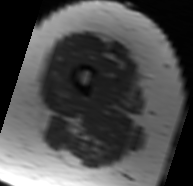
MRI of an extremity soft-tissue mass, one axial slice; position 11 of 91 along the scan axis; MR volume resampled by the dataset authors to the PET/CT grid (not the native acquisition matrix); 193 × 186 image matrix, field of view 188 × 182 mm. Female patient. Case-level facts recorded for this patient, not image findings: histological type: malignant solitary fibrous tumor; grade: intermediate; site of the primary tumour: right thigh.
Annotated regions visible in this slice (expert contour drawn on MRI and transferred to this co-registered scan by the dataset authors):
- gross tumour volume including surrounding oedema: bounding box [x1, y1, x2, y2] px = [79, 39, 125, 68]